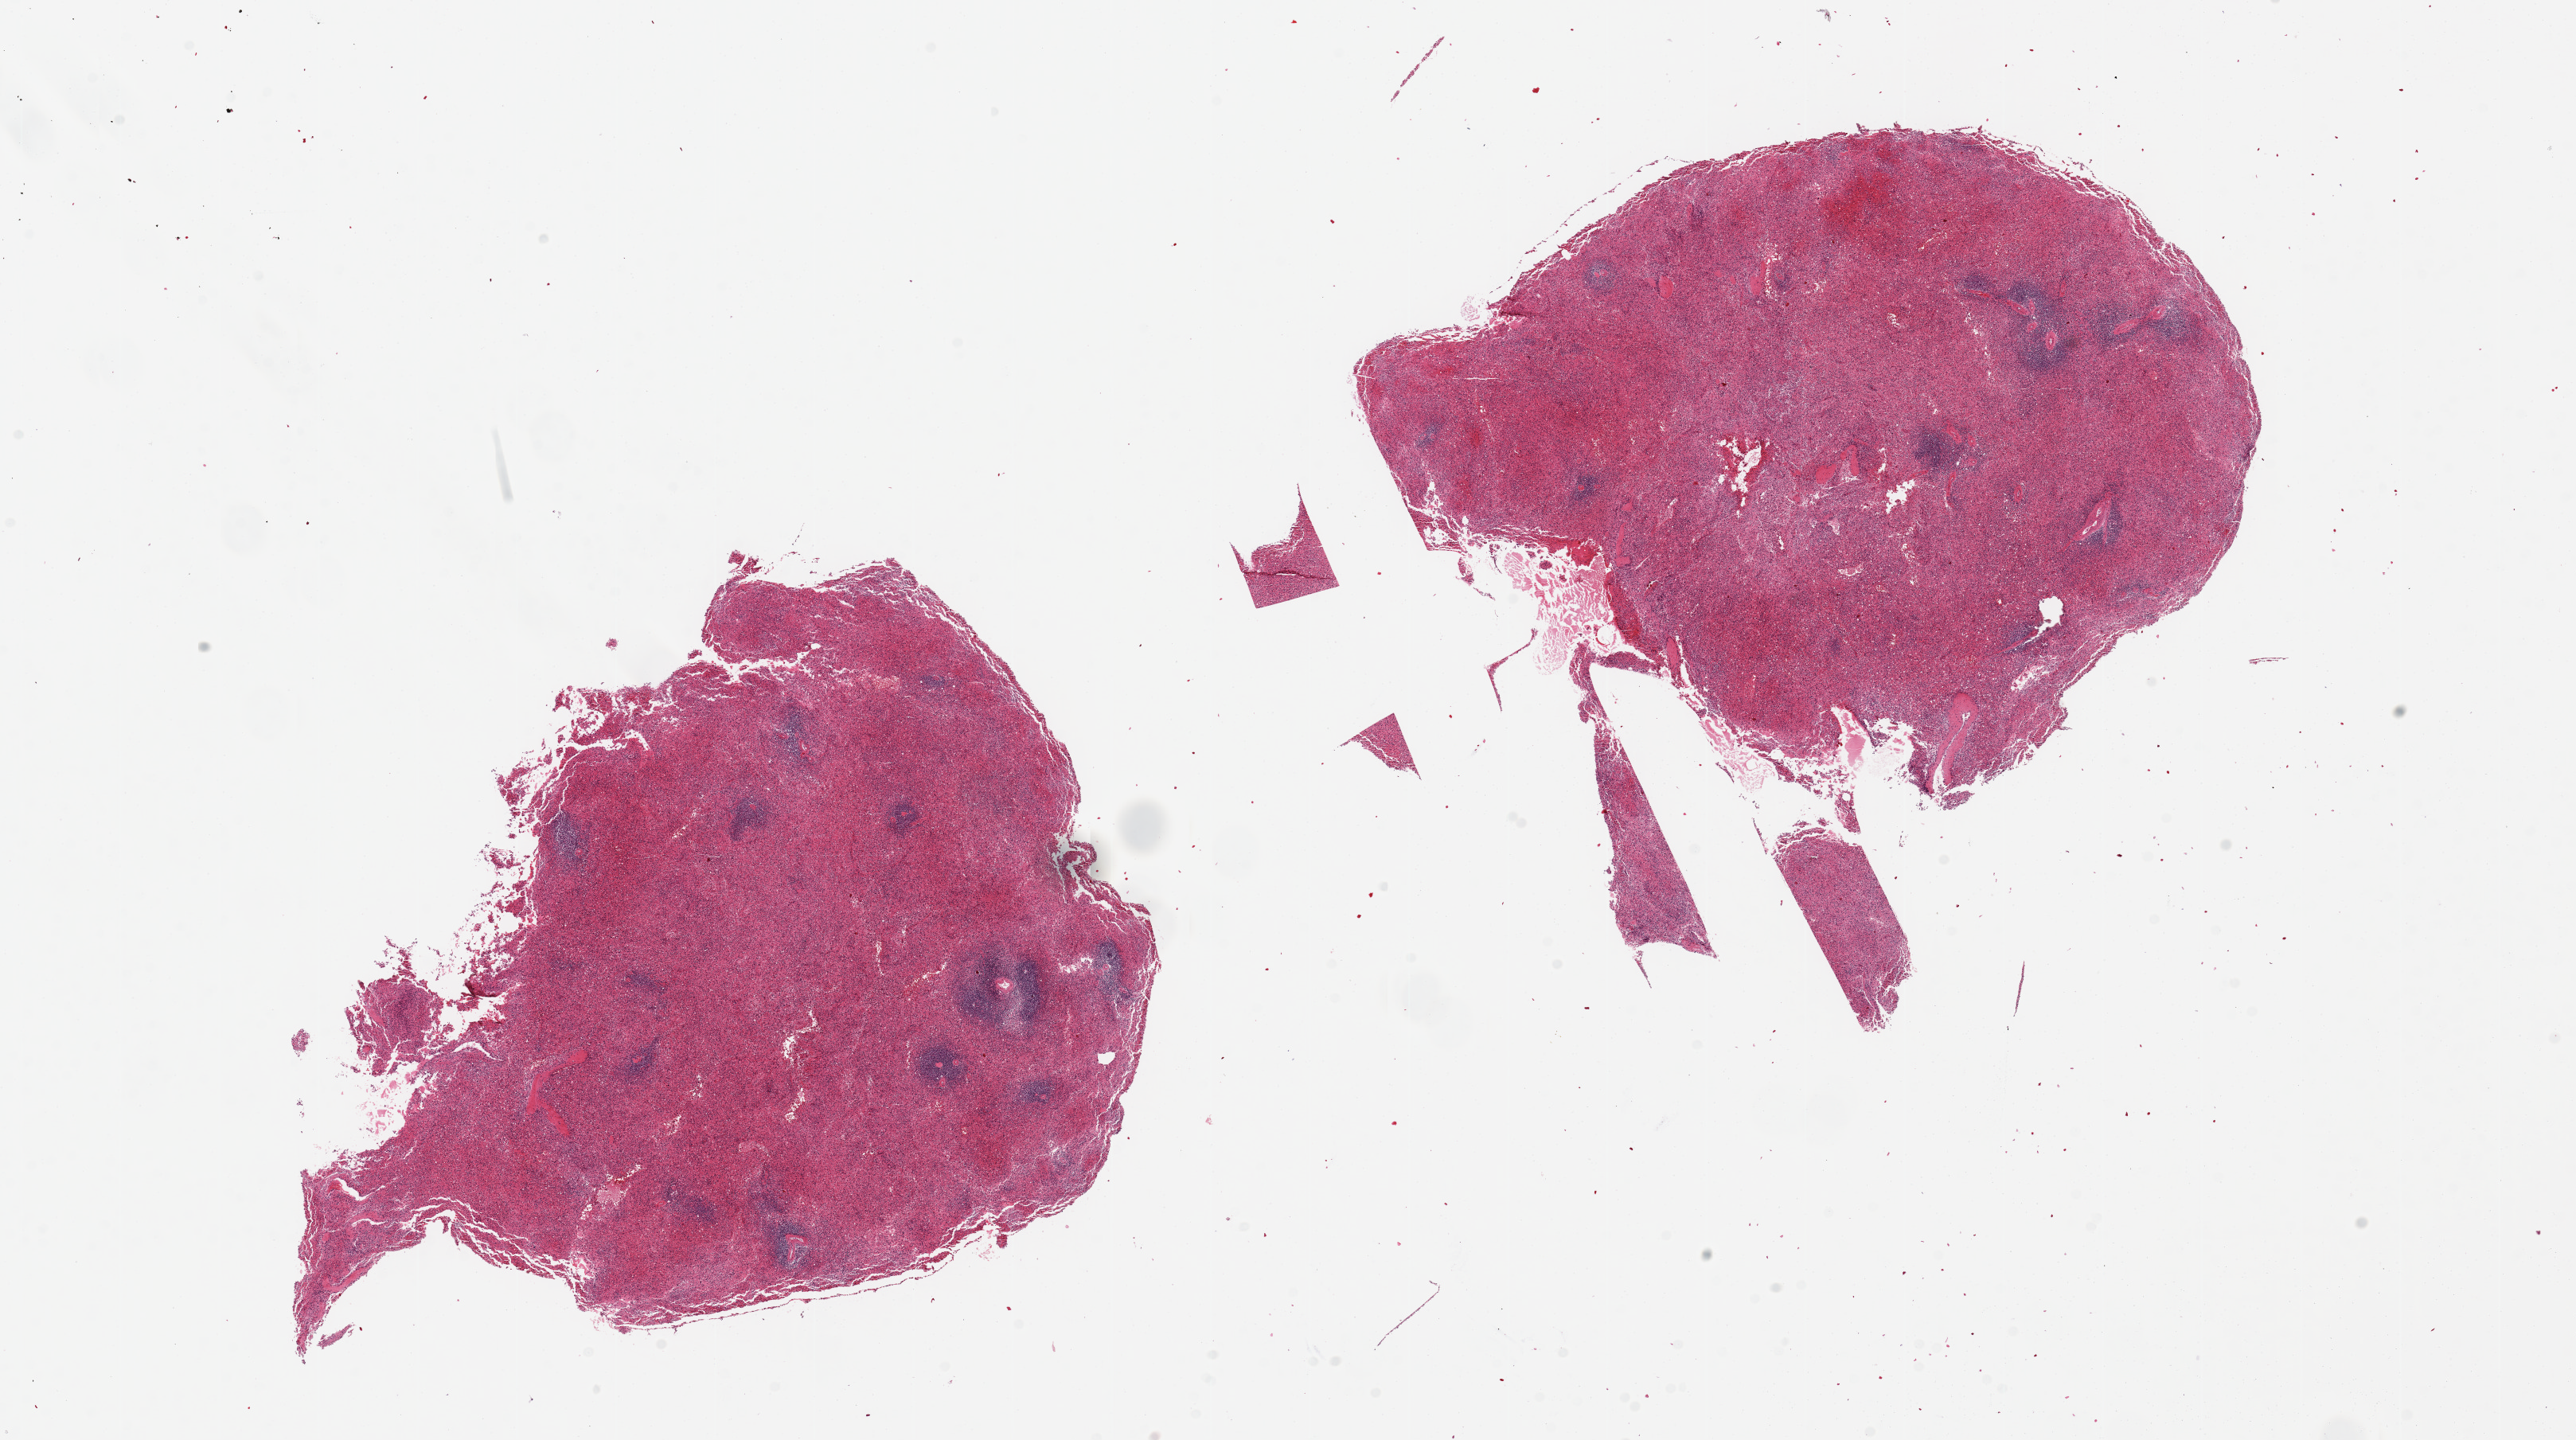
Digitized H&E-stained section — a low-resolution overview of the entire scanned area, about 25.6 x 14.3 mm, PAXgene-fixed paraffin-embedded (PFPE) section, sampled site (target tissue): spleen, donor tissue sample. Male donor.
Reviewer comment on this tissue sample: 2 pieces, 8.5x7 & 10x8mm; badly autolyzed, congested.